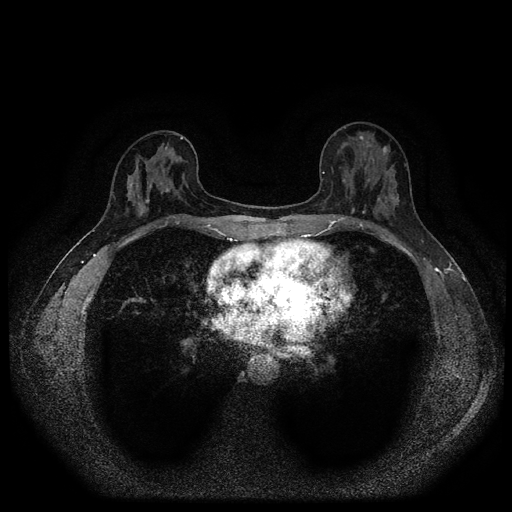
Breast MRI (dynamic contrast-enhanced, multi-phase), one axial slice; position 39 of 116 along the scan axis; dynamic contrast-enhanced series, time point 2 of 5 at this slice position (early post-contrast); 1.5 T; TE 2.7 ms, TR 5.4 ms; 512 × 512 image matrix. Female patient, age 42 years.
Outlined on this slice (semi-automatically segmented with operator editing):
- breast lesion (labelled benign in the annotation): box from (x=381, y=144) to (x=390, y=157) px